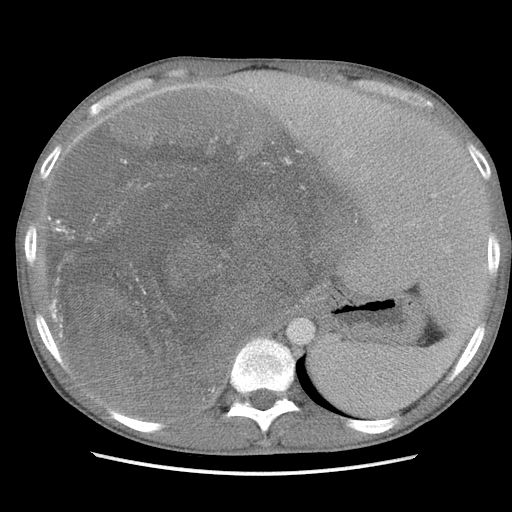
Contrast-enhanced abdominal CT, one axial slice. Slice 81 of 115 in the series (ordered by position). Soft-tissue window (W 400 / L 40 HU). 5 mm slice thickness. 512 × 512 image matrix. Male patient. From the clinical record (not read from this slice): diagnosis: adrenocortical carcinoma; tumour side: right adrenal; Ki-67 index: 13 %; stage (as recorded): 3.
Structures marked on this image (semi-automatic segmentation, software-assisted and operator-edited):
- mass: bounding box <52,95,354,417> (left, top, right, bottom; pixels)